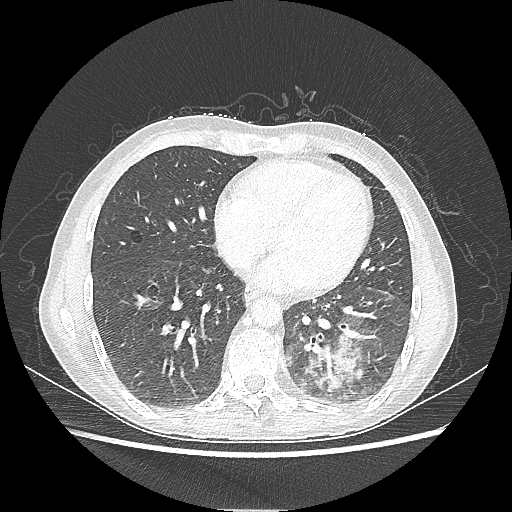
Chest CT, one axial slice. Position 84 of 220 along the scan axis. Reconstruction kernel LUNG. Lung window (W 1500 / L -600 HU). 1.25 mm slice thickness. 512 × 512 image matrix. Female patient, age 53 years. Case-level facts recorded for this patient, not image findings: clinical TNM (as recorded): T3 N0 M0.
Annotated regions visible in this slice (rectangle marked by the reading radiologist):
- lung tumour (recorded histology: adenocarcinoma): bounding box <300,326,363,396> (left, top, right, bottom; pixels)